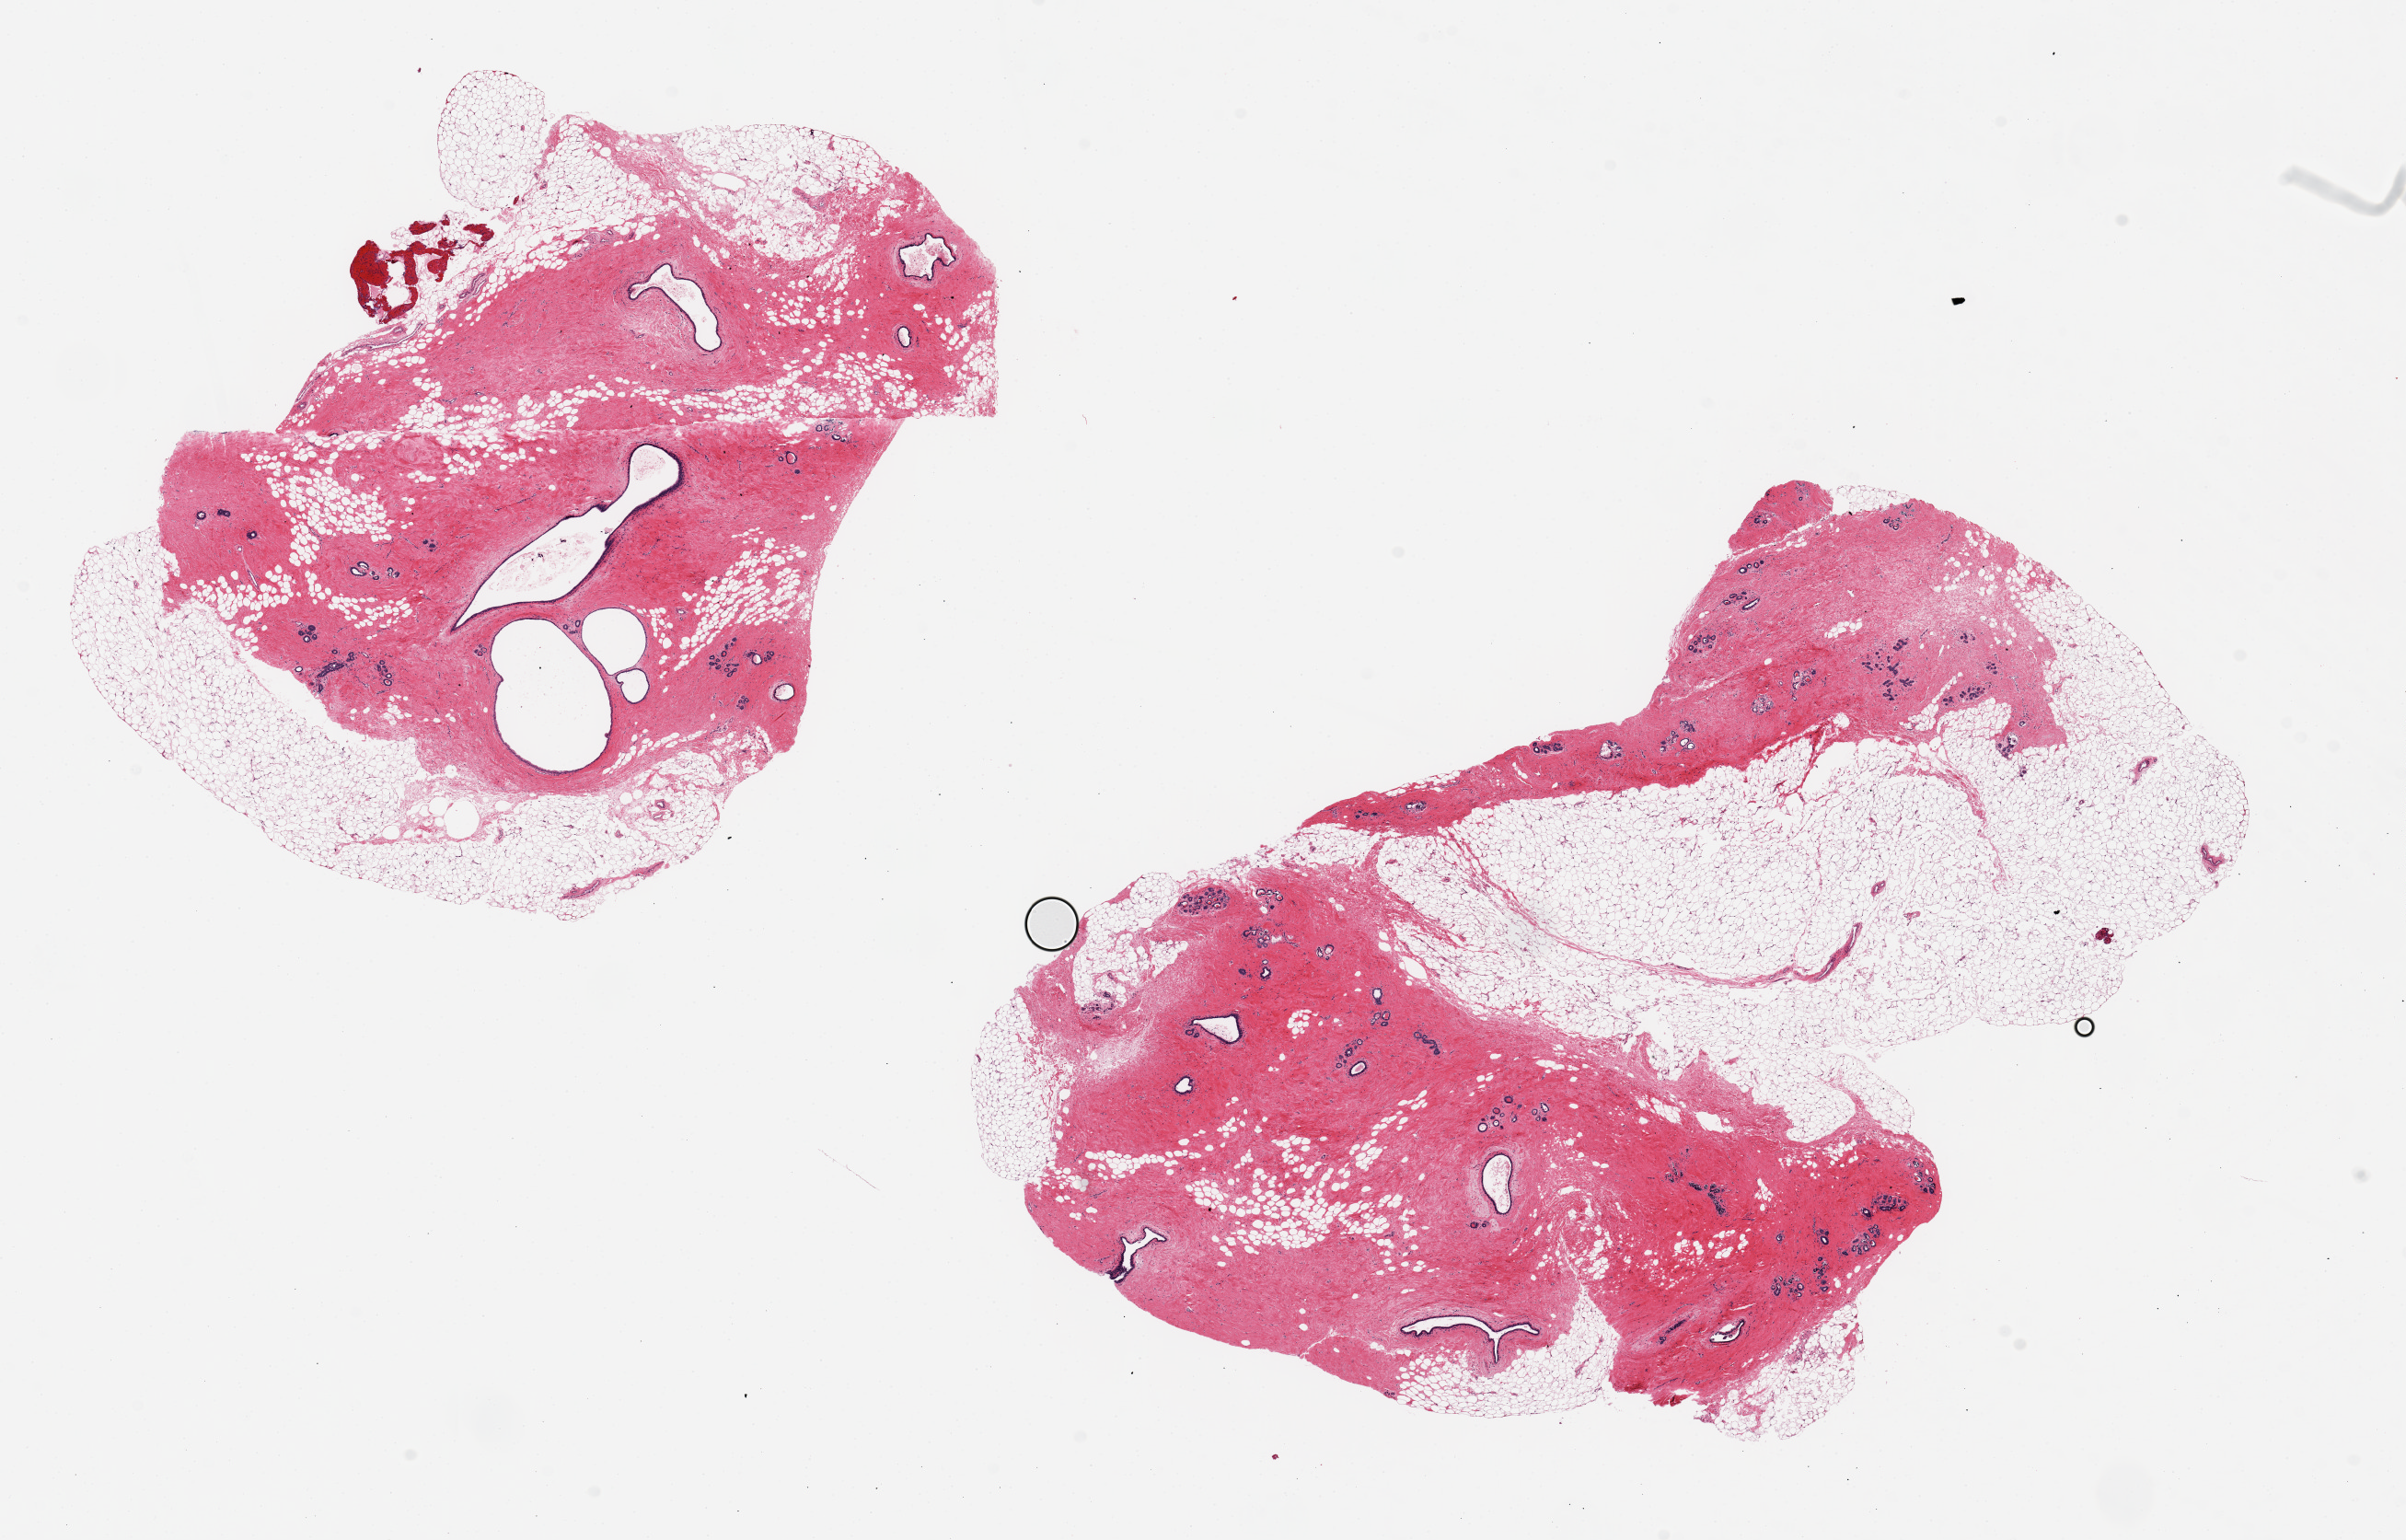
Digitized haematoxylin and eosin-stained section — low-resolution overview of the scanned area, about 20.7 x 13.2 mm (slide scanned at 20x). PAXgene-fixed, paraffin-embedded tissue. Target tissue: breast. Donor tissue sample. Donor: female.
Reviewer comment on this tissue sample: 2 pieces 9x7 & 8x5 mm; fibrocystic changes; ~20 & 40% adipose admixed.